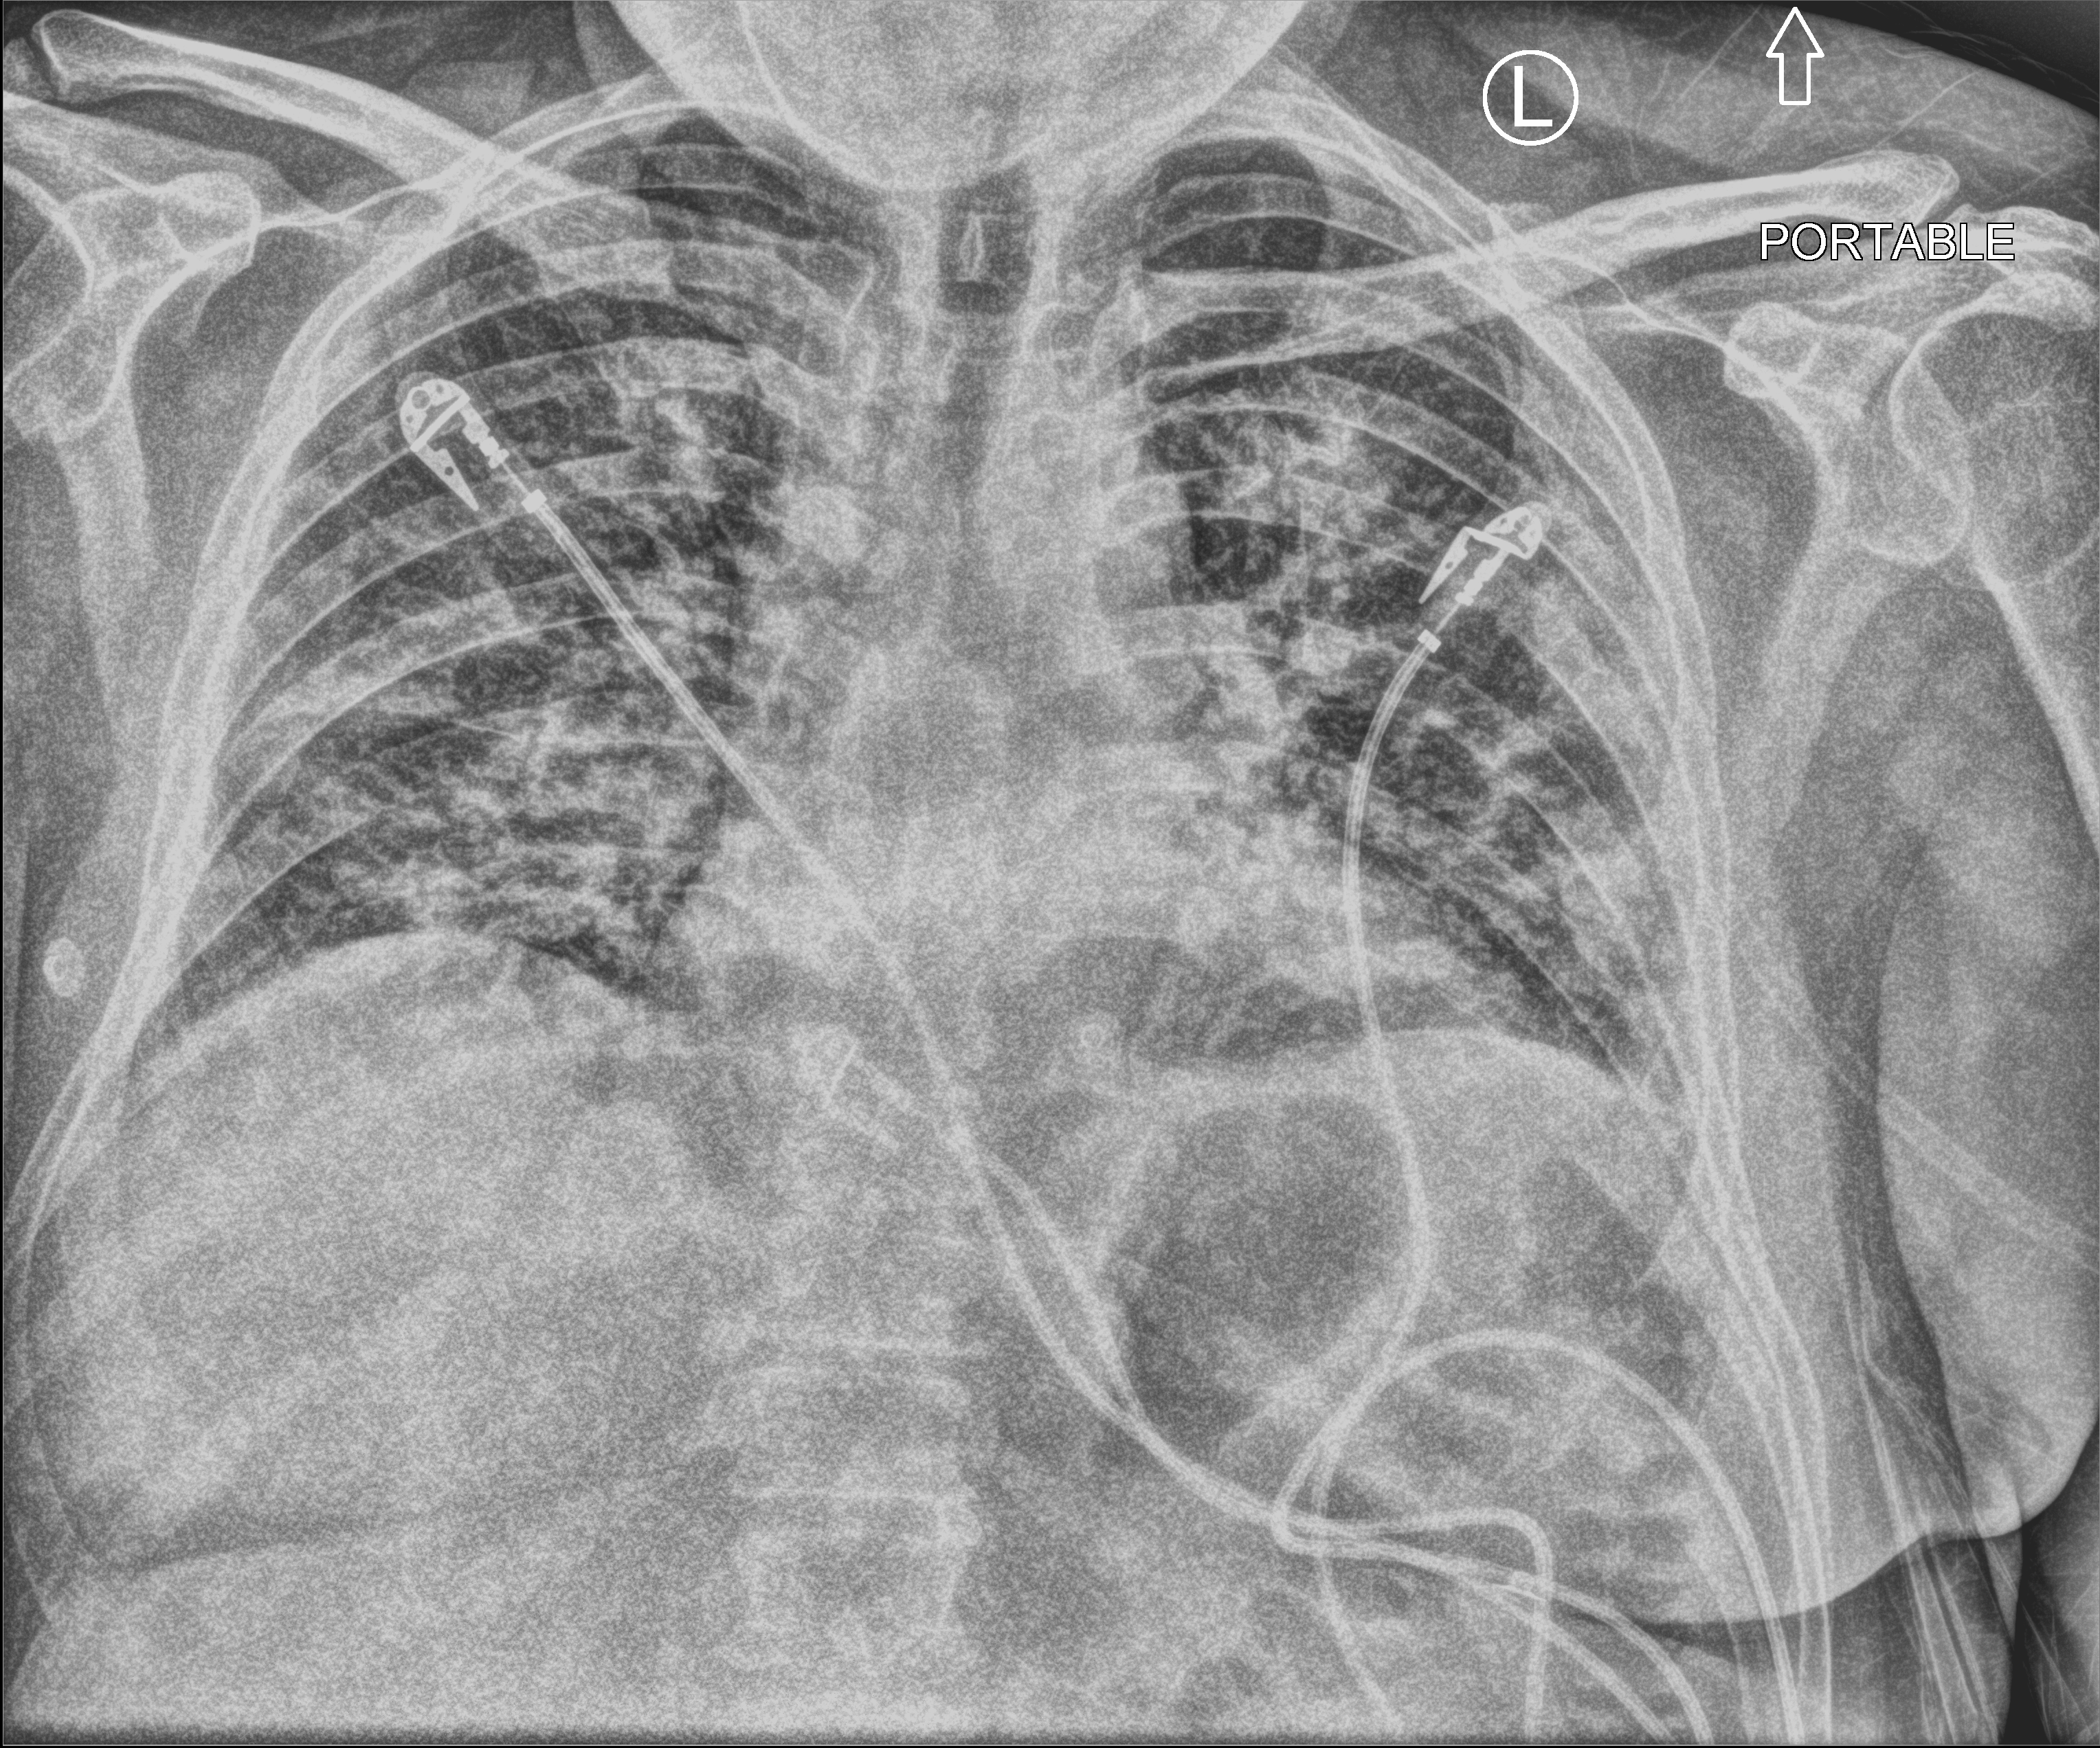
Bedside chest radiograph (computed radiography); anteroposterior (AP) projection. Patient hospitalised with COVID-19; male, aged 18–59 years.
Hospital-stay facts (about this admission, not read from this image; timing relative to this image not recorded): length of hospital stay: 12 days.